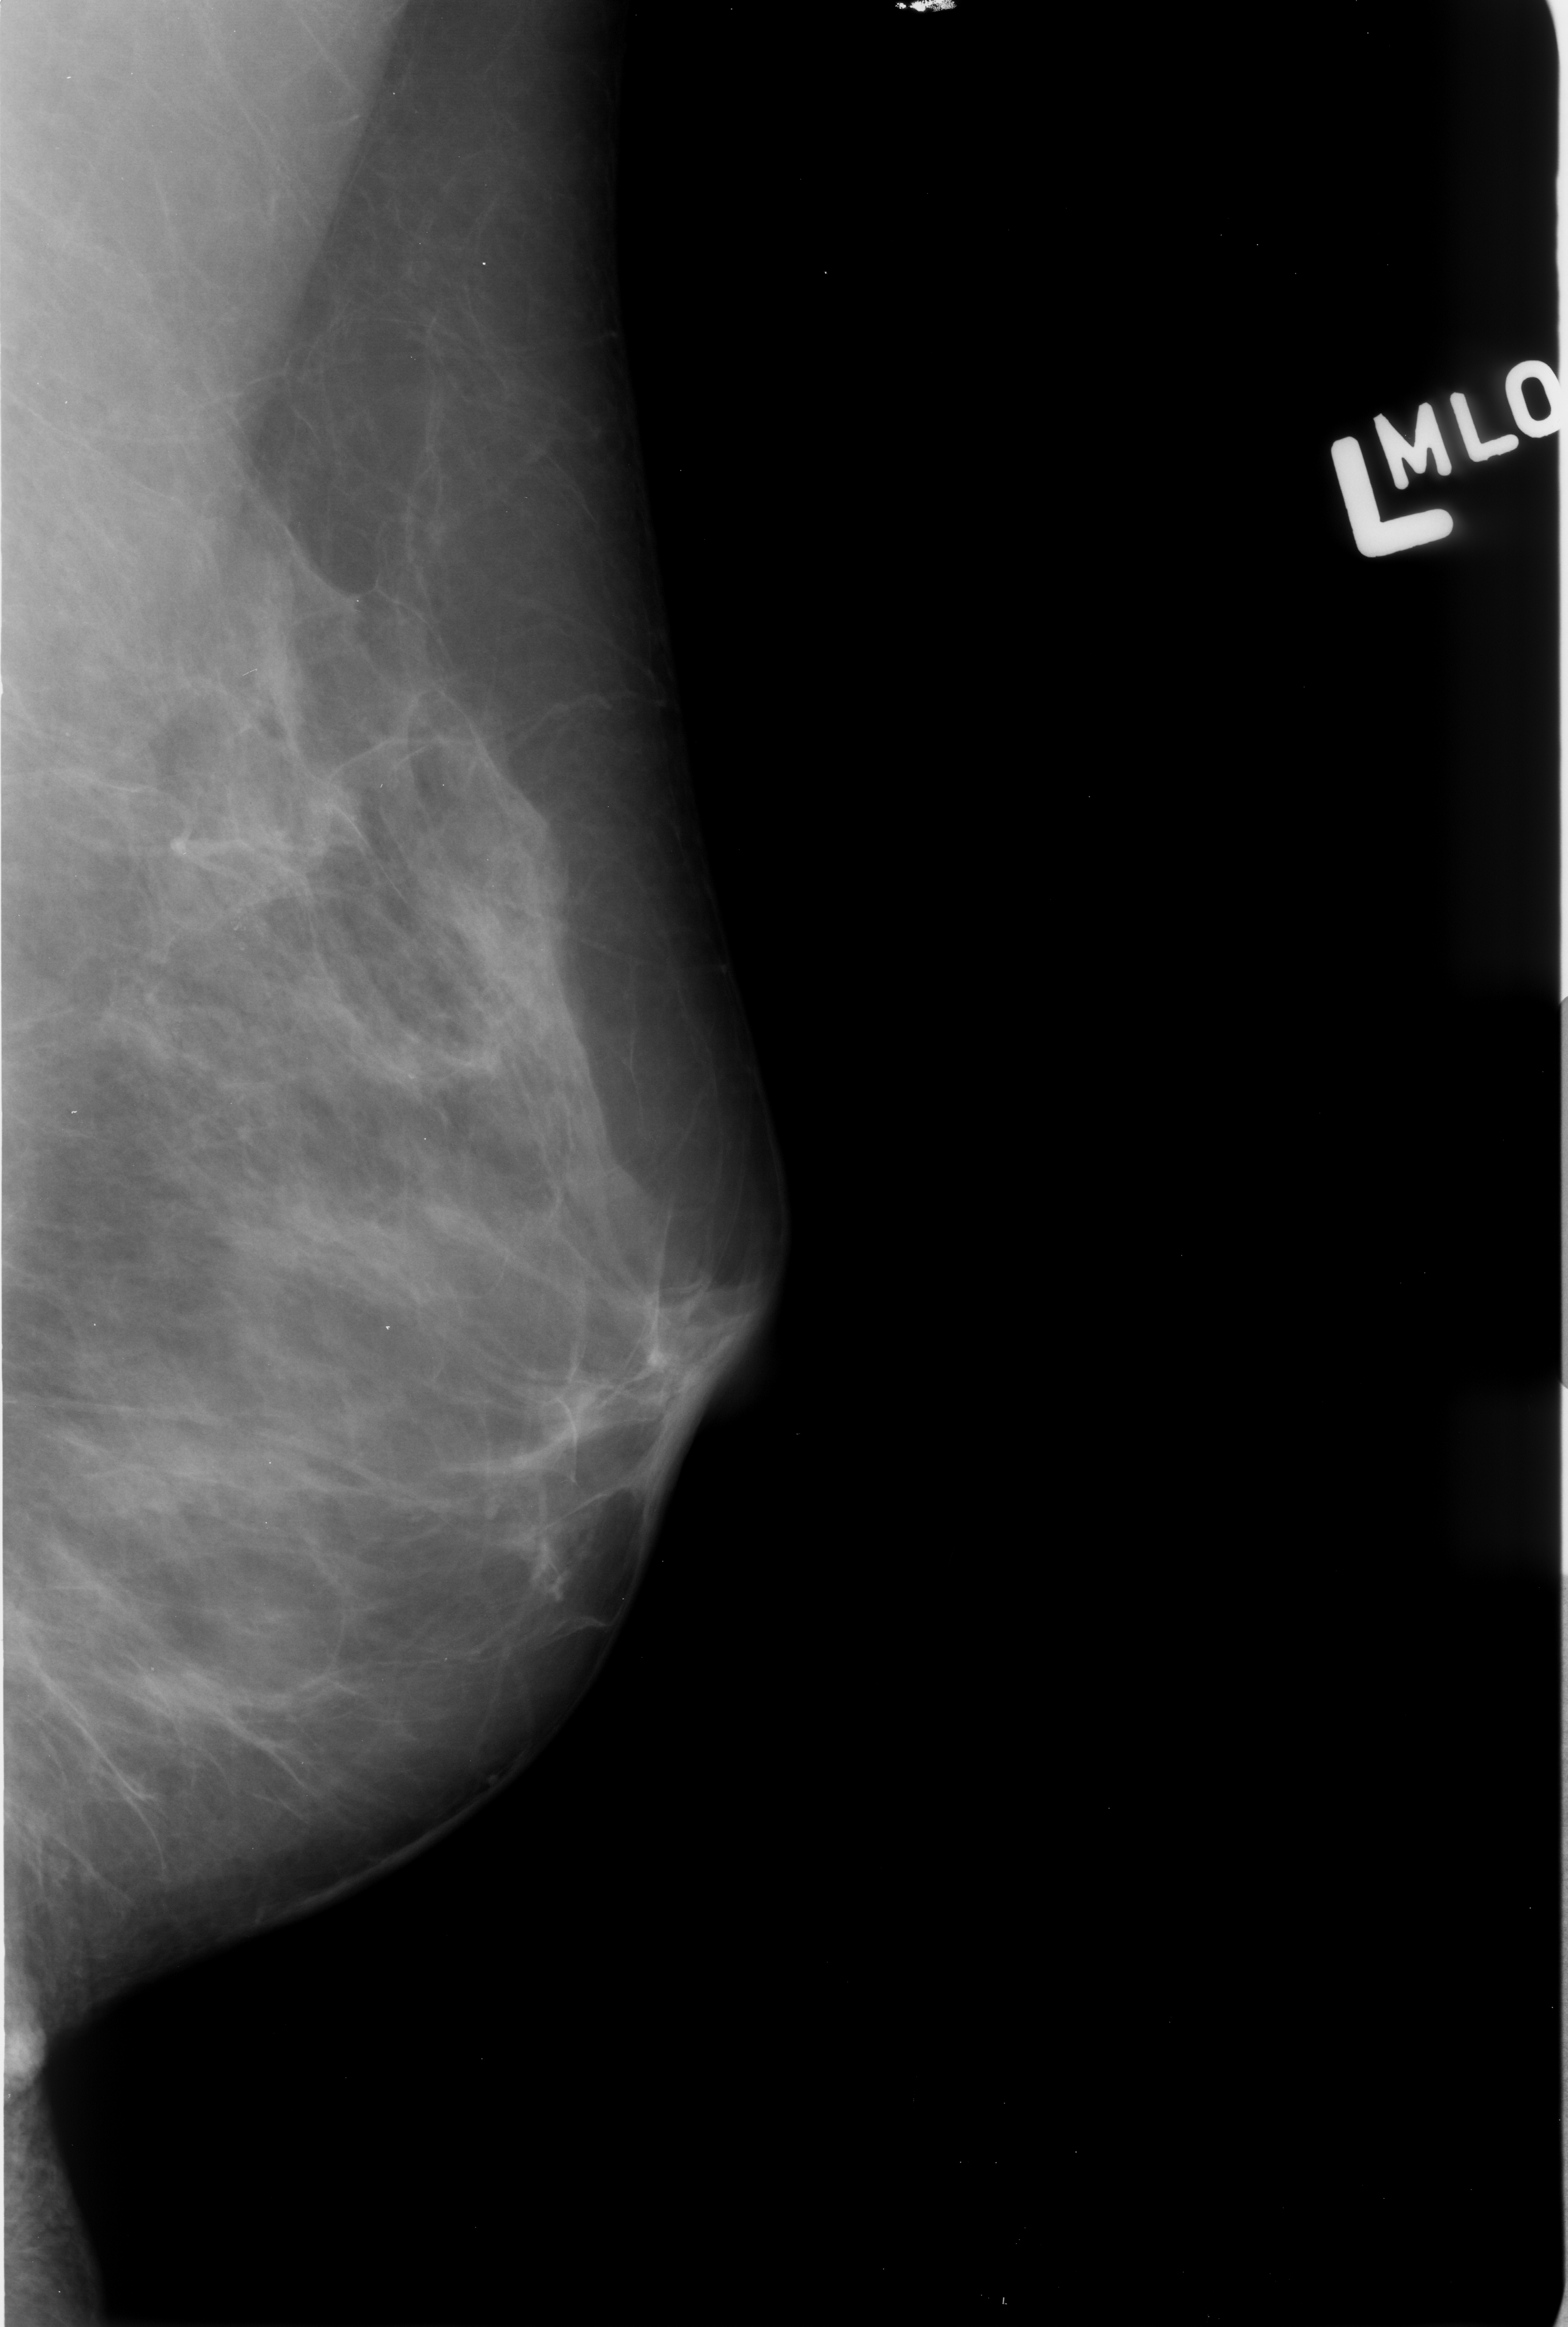
Scanned film-screen mammogram; left breast; MLO view; 1568 × 2327 image matrix.
Expert-marked regions of interest on this image (one box per marked abnormality):
- calcifications, morphology pleomorphic, distribution clustered; BI-RADS assessment category 4; pathology (as recorded): benign: bounding box [x1, y1, x2, y2] px = [161, 887, 271, 955]